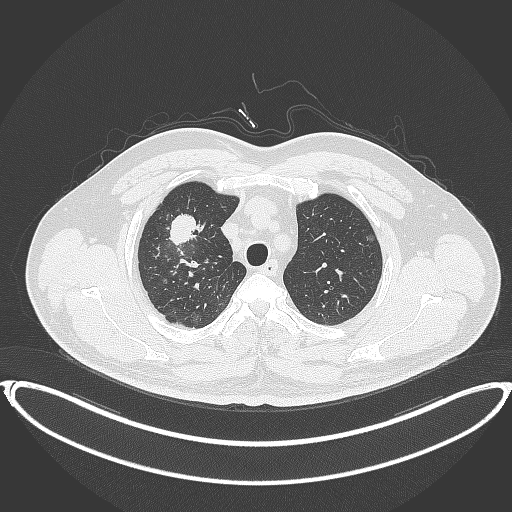
Chest CT, one axial slice; position 312 of 399 along the scan axis; reconstruction kernel B70f; lung window (W 1500 / L -600 HU); 512 × 512 image matrix, field of view 445 × 445 mm. Patient: male, 53 years. From the clinical record (not read from this slice): clinical TNM (as recorded): T2a N0 M0.
Outlined on this slice (rectangle marked by the reading radiologist):
- lung tumour (recorded histology: adenocarcinoma): bounding box [x1, y1, x2, y2] px = [167, 210, 207, 249]